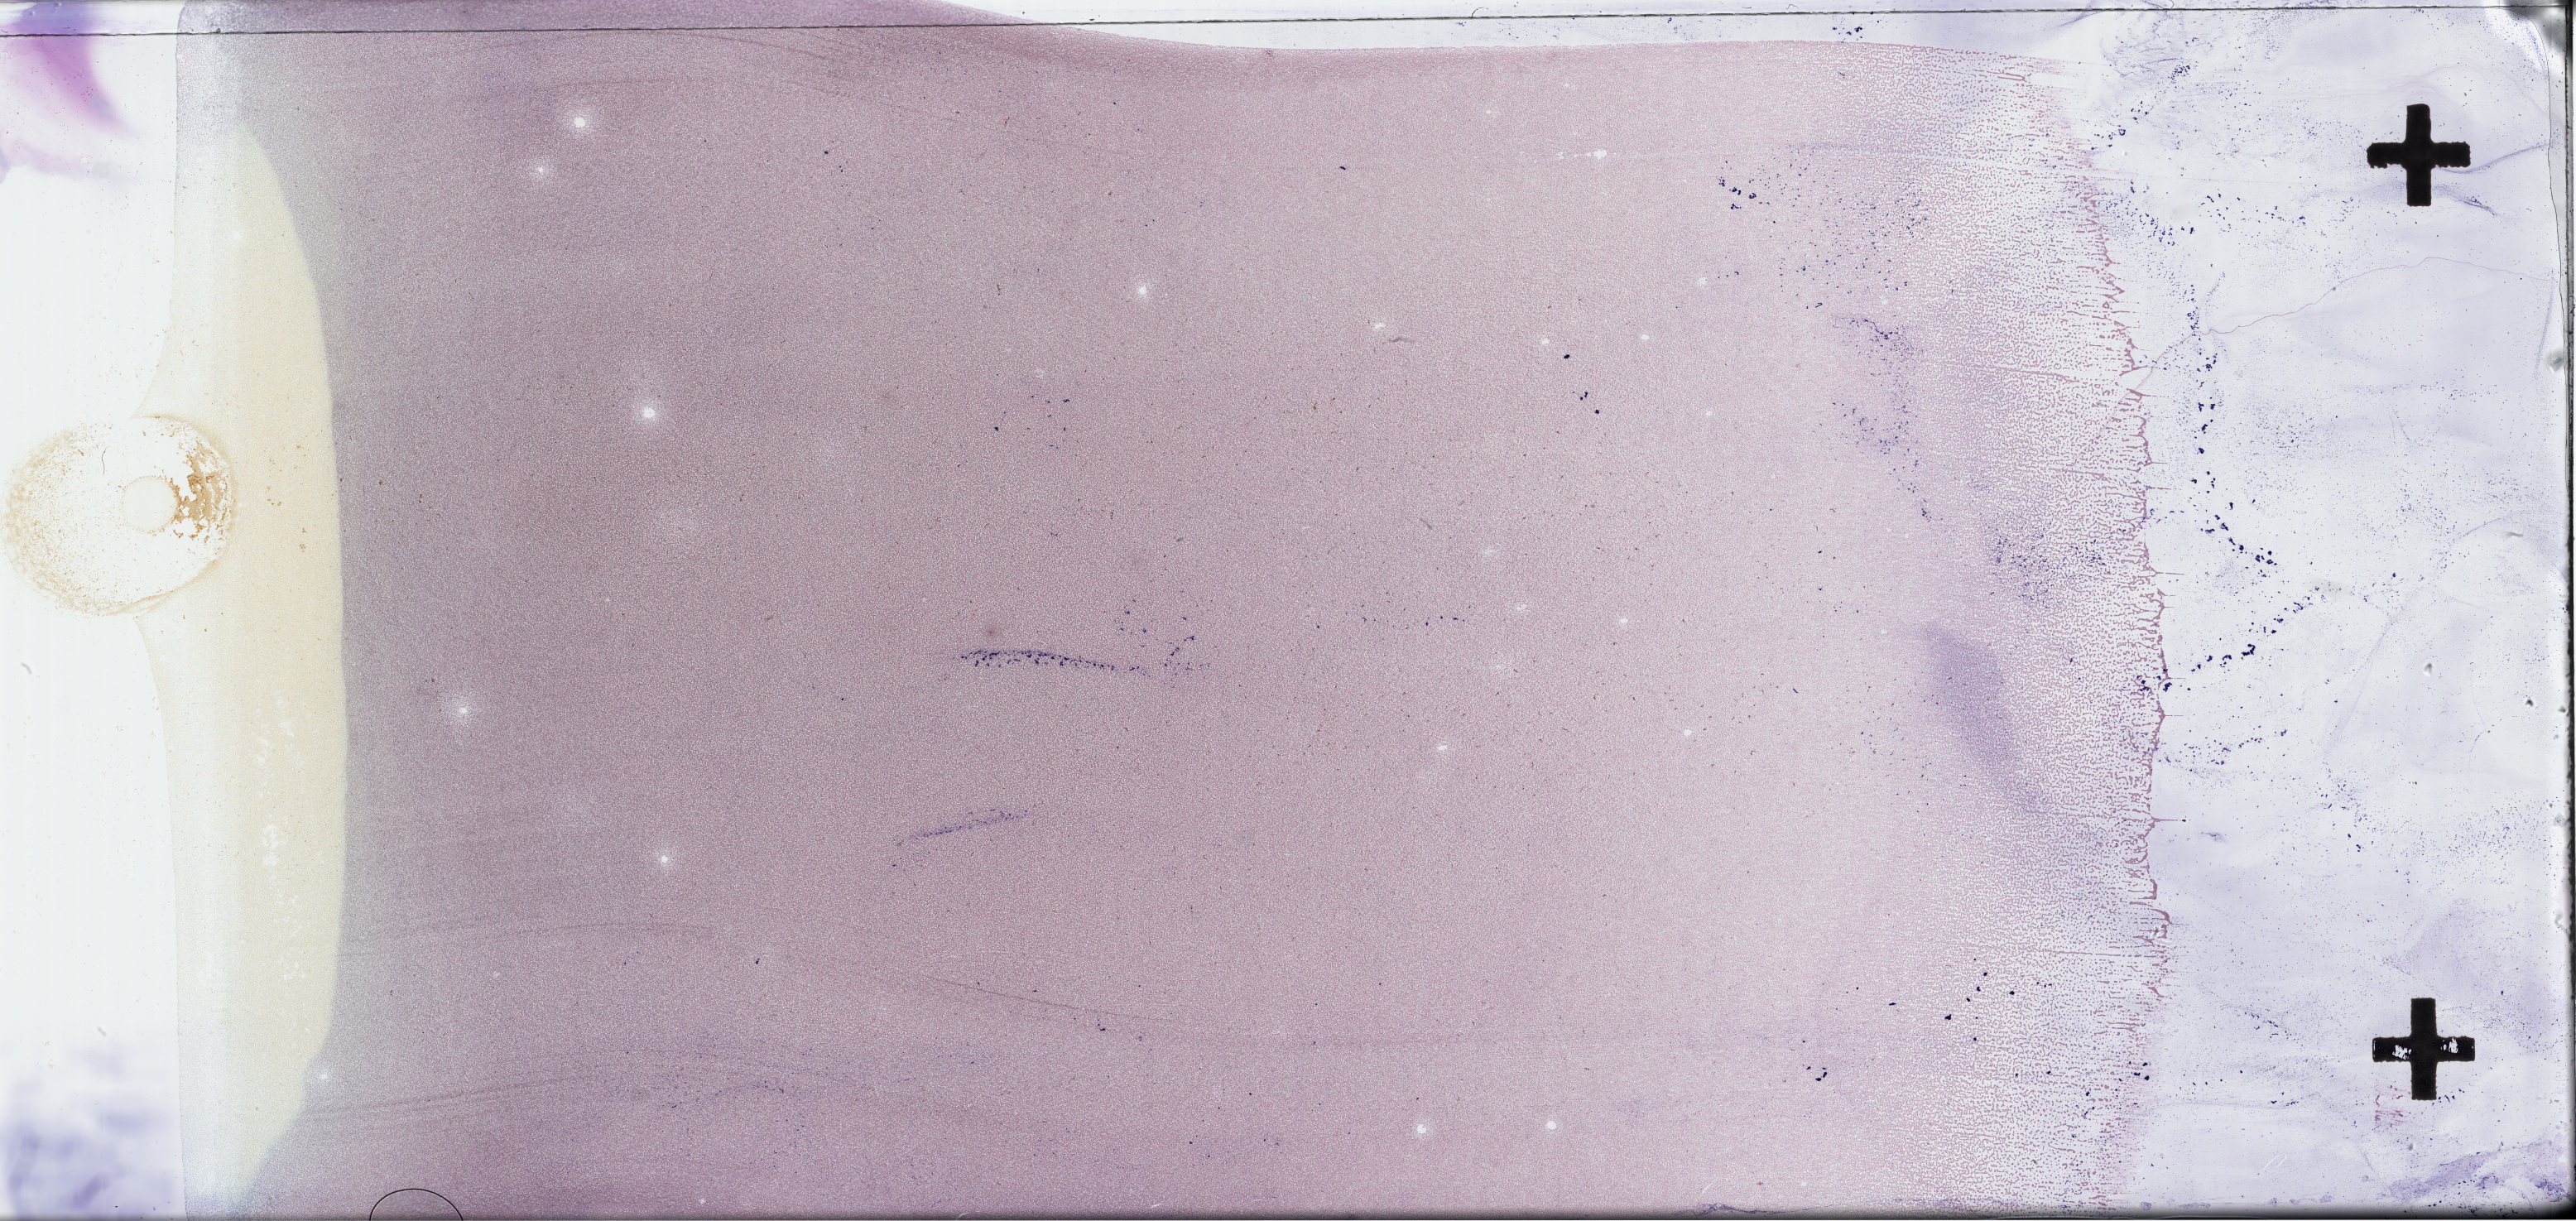
Wright–Giemsa-stained bone marrow smear, whole-slide image, a low-resolution overview of the entire scanned area, about 50.3 x 23.8 mm; EDTA-anticoagulated smear; specimen time point: collected at baseline (before treatment). Patient sex: female.
Patient diagnosis: Plasma Cell Myeloma.